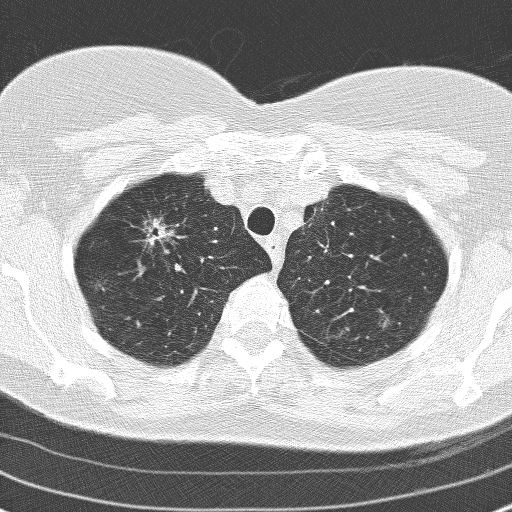
Low-dose screening chest CT, one axial slice. Position 130 of 160 along the scan axis. Lung window (W 1500 / L -600 HU). 3.2 mm slice thickness. 512 × 512 image matrix, field of view 313 × 313 mm.
Annotated regions visible in this slice (expert manual segmentation):
- lesion 1 (tumor, upper lobe of right lung): bounding box <151,222,169,242> (left, top, right, bottom; pixels)